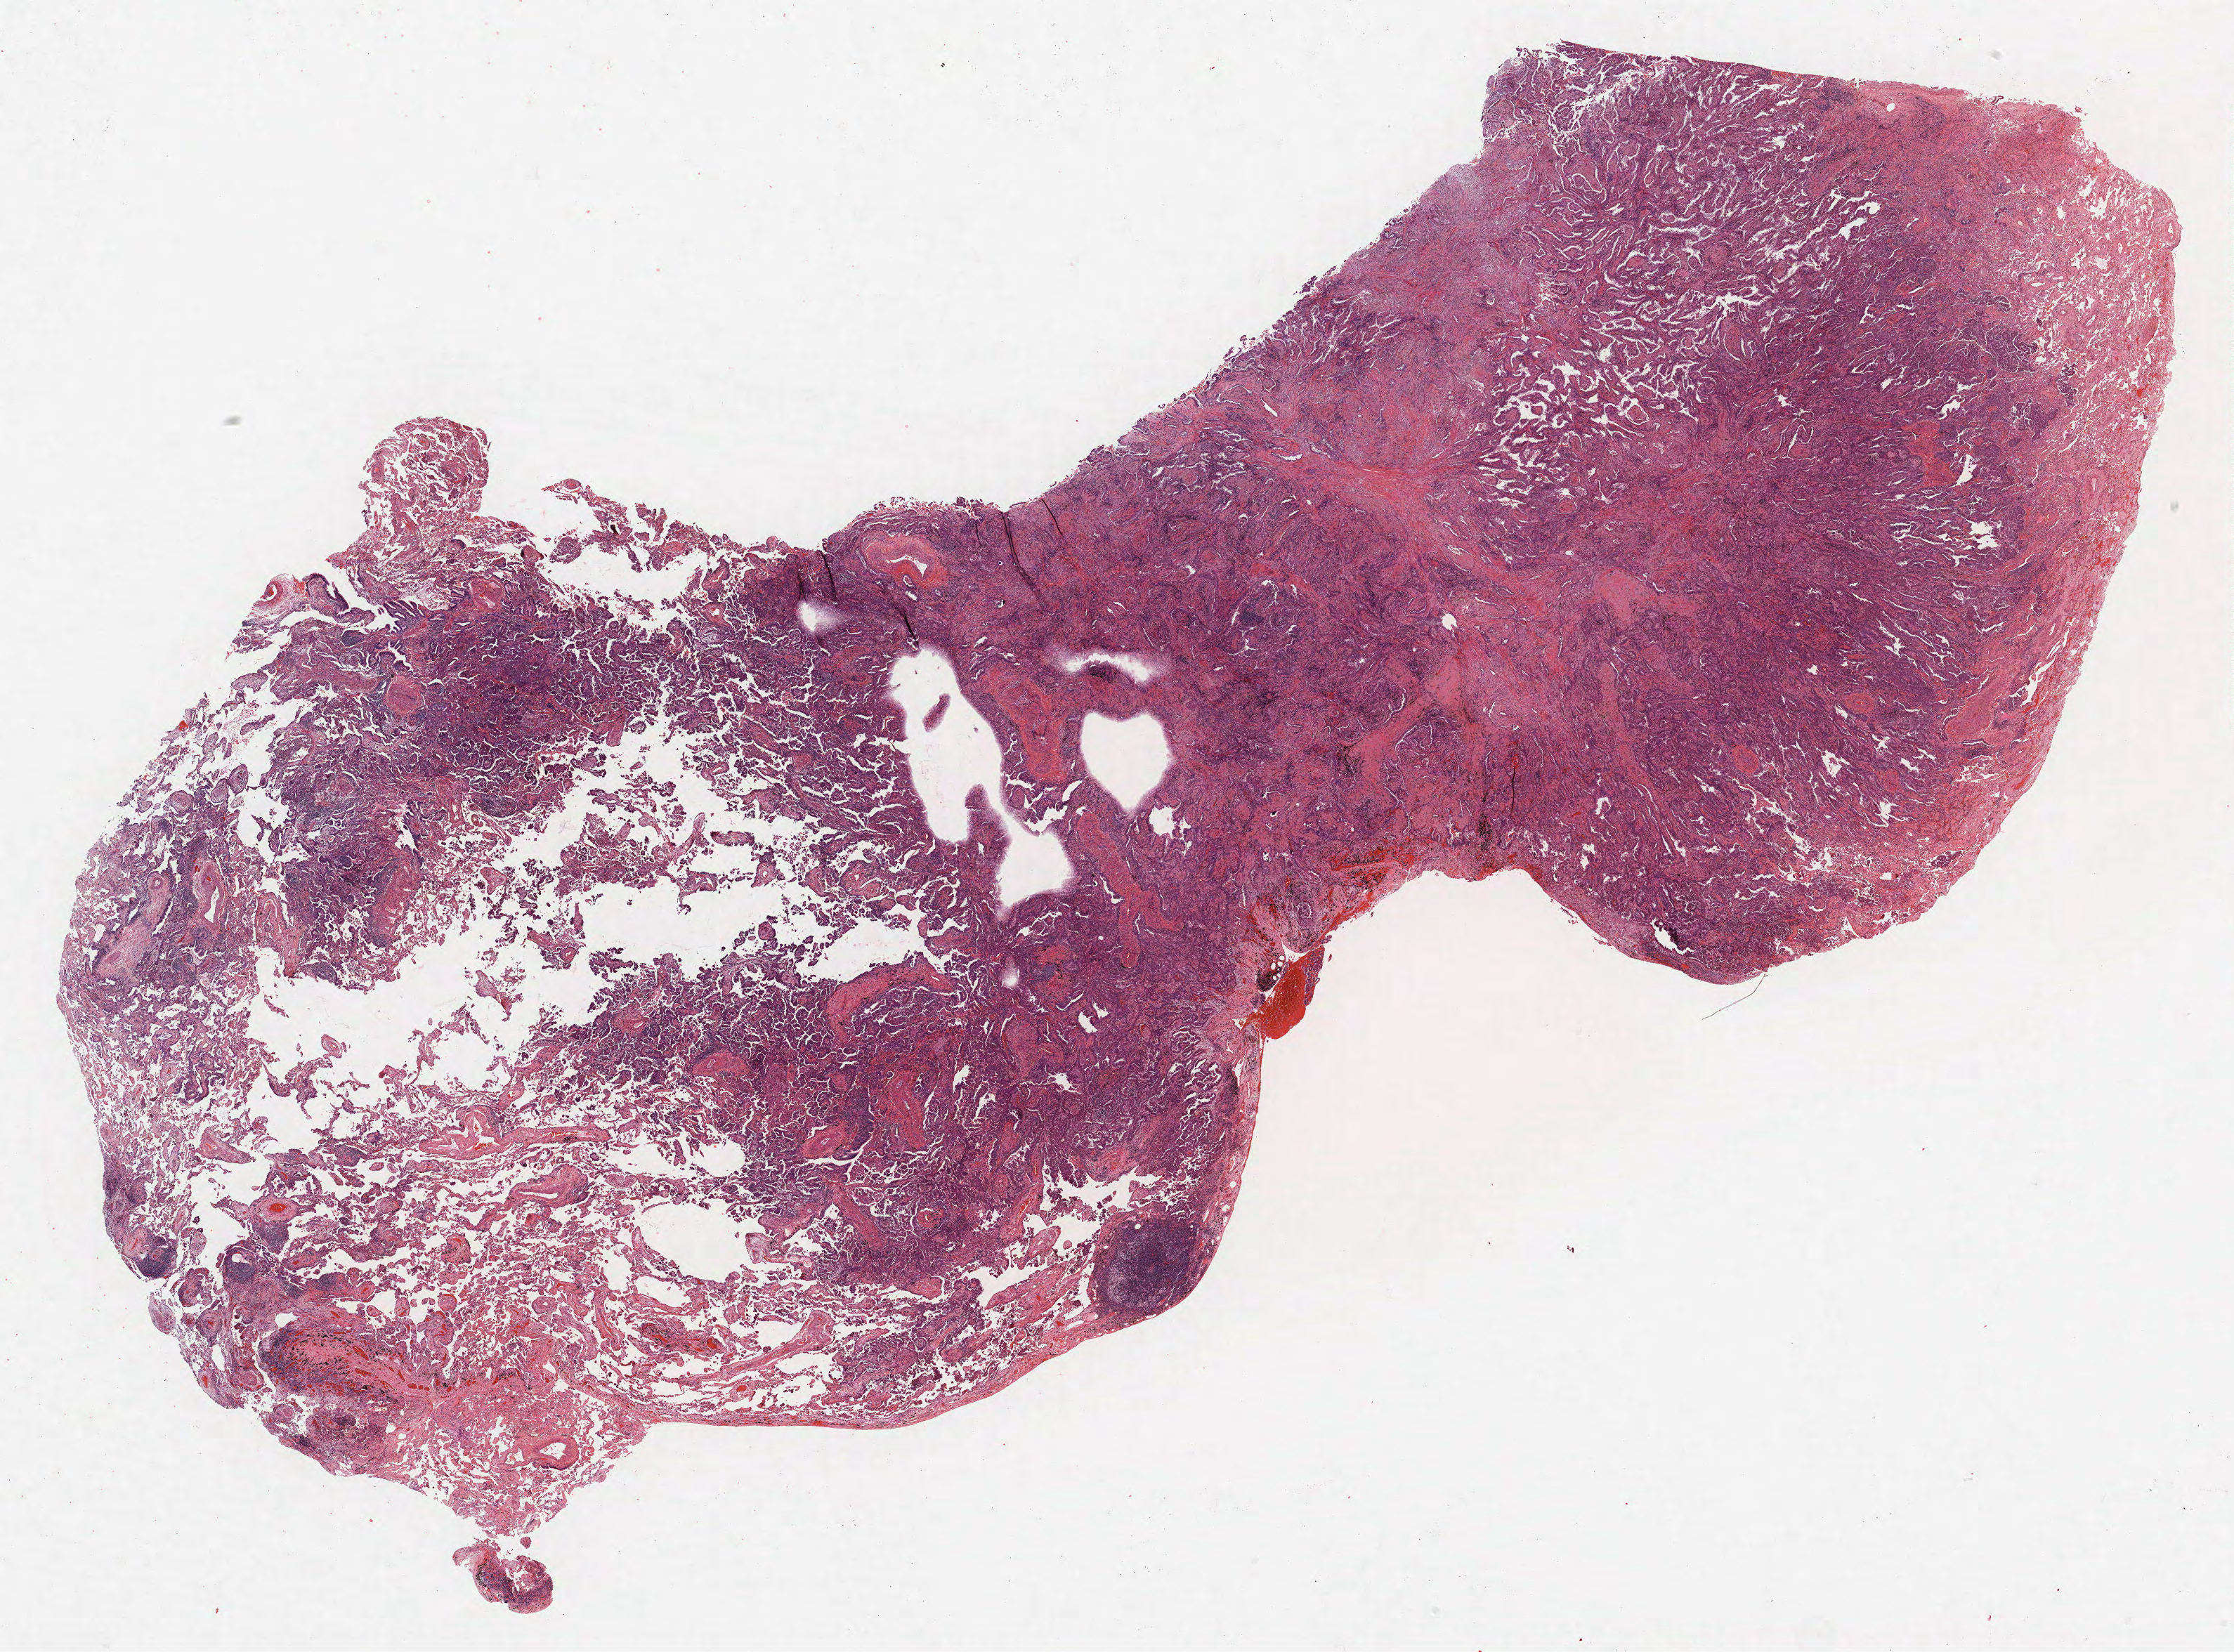
H&E-stained whole-slide image, whole scanned area (about 25.4 x 18.8 mm, from a 40x scan) shown as a low-resolution overview. Formalin-fixed paraffin-embedded (FFPE) section. Lung. Male patient, aged 60 at enrolment. Former smoker at enrolment.
Participant's lung-cancer diagnosis: Neoplasm, malignant.